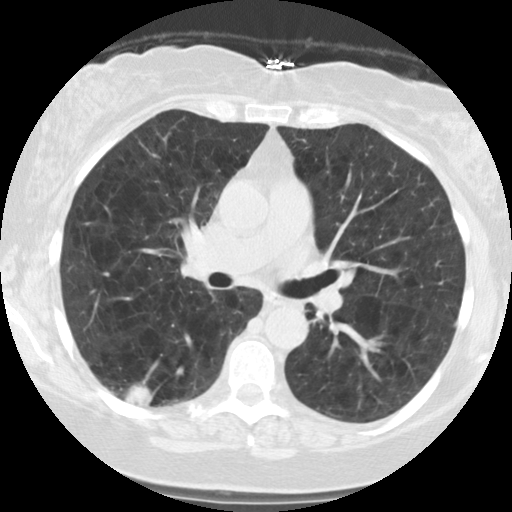
Low-dose screening chest CT, one axial slice; position 67 of 122 along the scan axis; reconstruction kernel STANDARD; 140 kVp; lung window (W 1500 / L -600 HU); 2.5 mm slice thickness; 512 × 512 image matrix.
Outlined on this slice (outlined manually by an expert reader):
- lesion 1 (tumor, lower lobe of right lung): bounding box (x1, y1, x2, y2) in pixels: (124, 384, 154, 407)